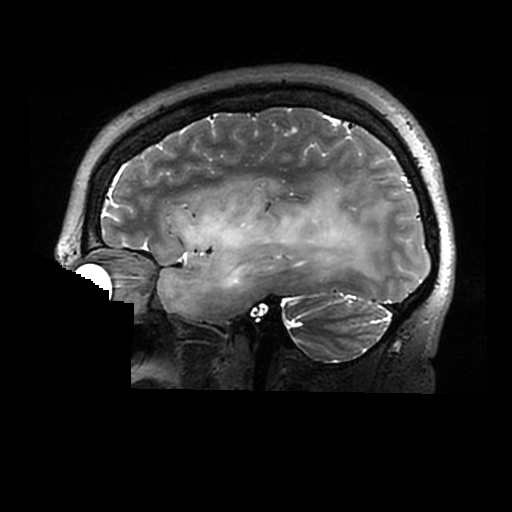
Brain MRI from a brain-tumour surgery series, one sagittal slice; 0.6 mm slice thickness; 512 × 512 image matrix, field of view 240 × 240 mm. From the clinical record (not read from this slice): histopathology: Astrocytoma; WHO grade: 2; IDH mutation: yes.
Structures marked on this image (manually delineated by an expert):
- tumour: box from (x=156, y=181) to (x=384, y=314) px